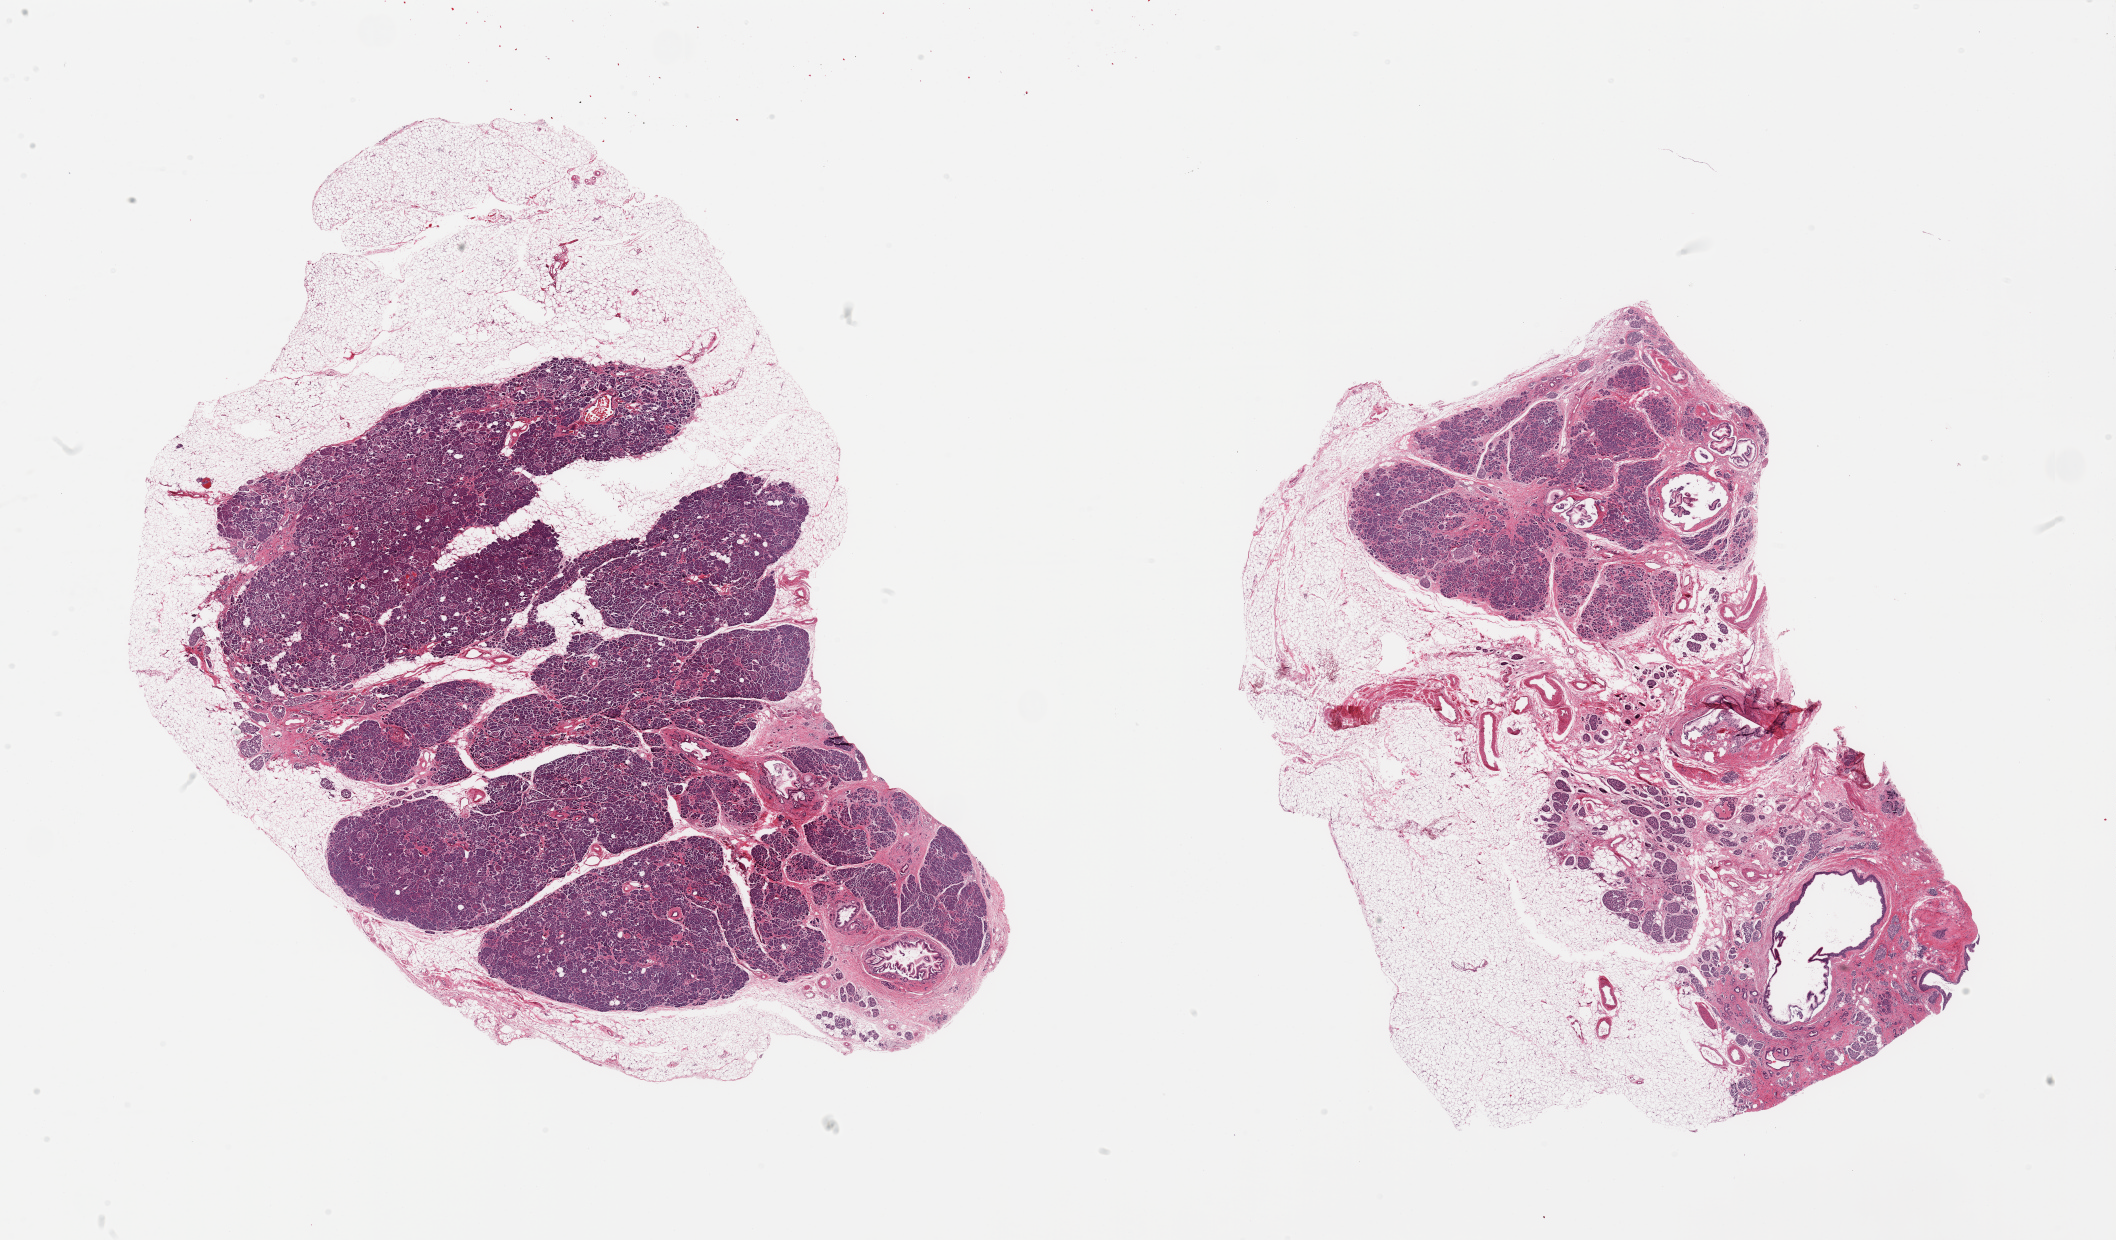
Haematoxylin and eosin whole-slide image, brightfield, a low-resolution overview of the entire scanned area, about 33.5 x 19.6 mm (acquisition: 20x scan). PAXgene-fixed paraffin-embedded (PFPE) section. Sampled site (target tissue): pancreas. Tissue donor sample. Donor sex: female.
Pathologist's review note for this sample: 2 pieces; 1 piece has 30% external fat content; other has 40% external fat with 60% of exocrine parenchyma scarred leaving numerous end0crine islets; PanIN 1b.